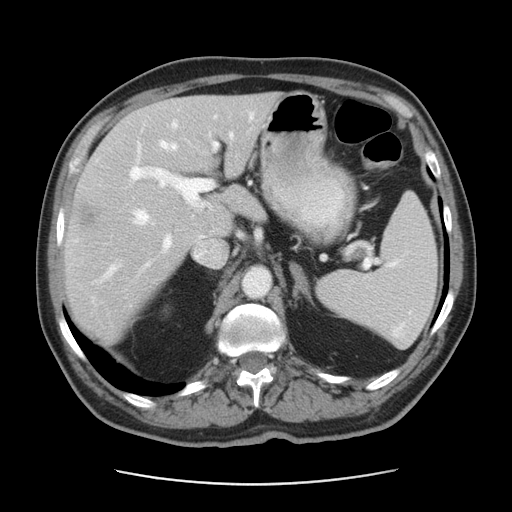
Contrast-enhanced abdominal CT, one axial slice. Position 28 of 42 along the scan axis. Reconstruction kernel STANDARD. 120 kVp. Intravenous contrast given. Soft-tissue window (W 400 / L 40 HU). 512 × 512 image matrix, field of view 370 × 370 mm. Male patient, age 73 years. Case-level facts recorded for this patient, not image findings: diagnosis: colorectal cancer liver metastases, imaged before liver resection.
Outlined on this slice (outlined manually by an expert reader):
- hepatic veins: box from (x=101, y=118) to (x=252, y=281) px
- liver: (x=65, y=96)–(x=276, y=340)
- planned liver remnant (the part of the liver to remain after resection): (x=112, y=96)–(x=276, y=236)
- portal vein (with intrahepatic branches): (x=131, y=142)–(x=218, y=269)
- liver metastasis: (x=81, y=203)–(x=101, y=226)